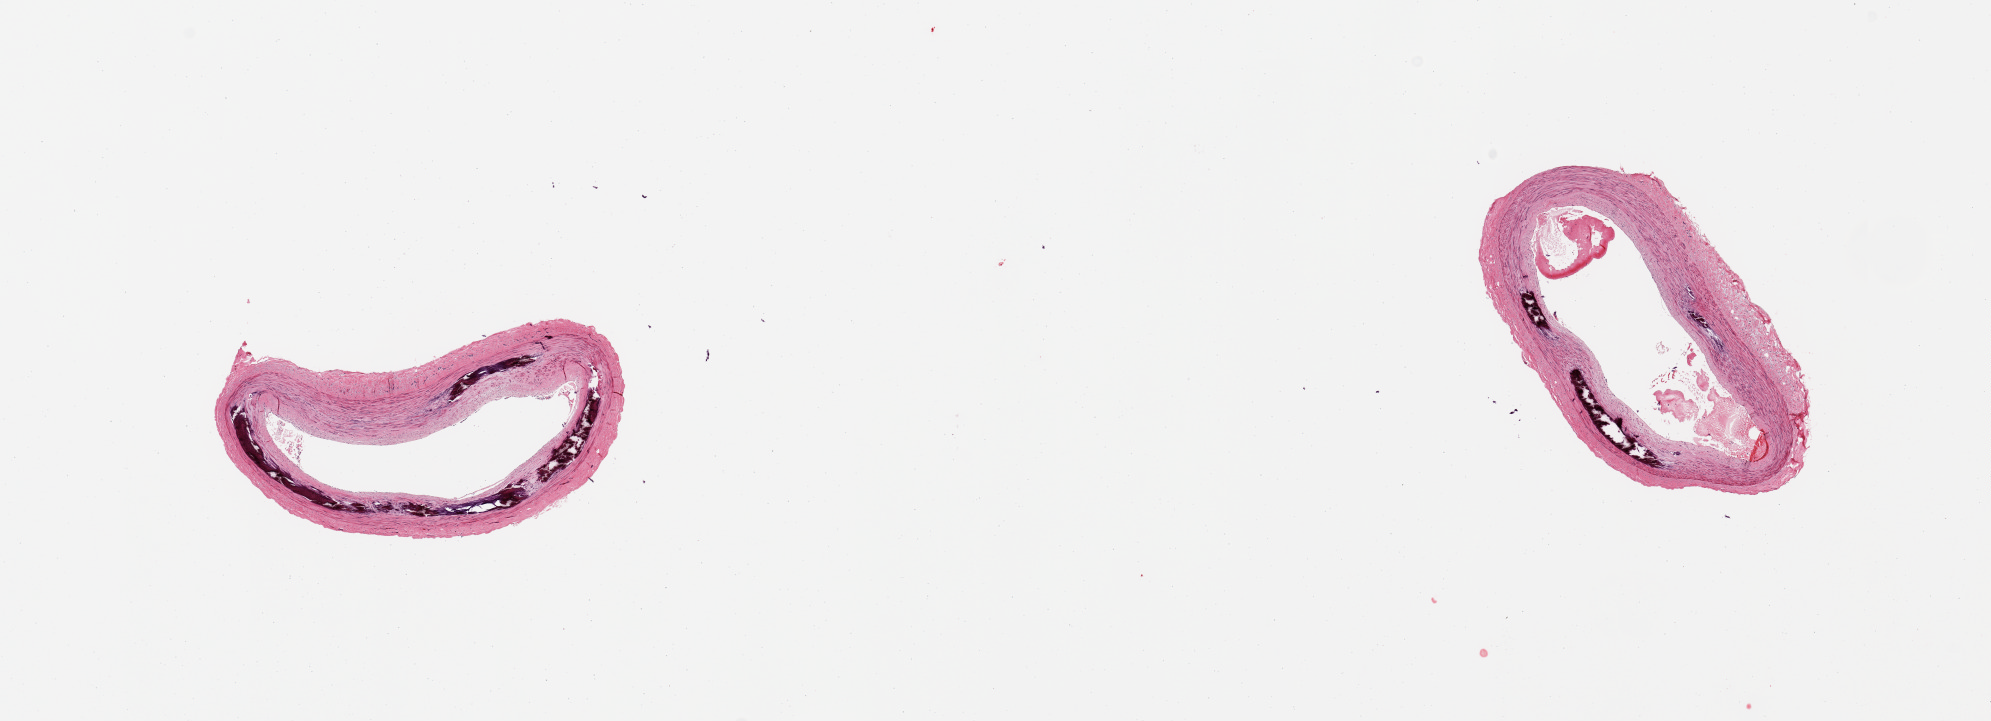
Whole-slide image, hematoxylin and eosin (H&E) stain, brightfield, whole scanned area (about 15.8 x 5.7 mm, acquisition: 20x scan) shown as a low-resolution overview. PAXgene-fixed paraffin-embedded (PFPE) section. Section of tibial artery (target tissue). Tissue donor sample. Donor: female.
Reviewer comment on this tissue sample: 2 pieces; atheromatous plaque and extensive medial calcification.